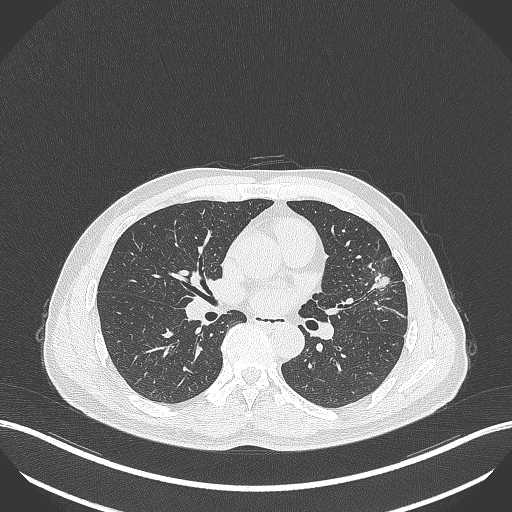
Chest CT, one axial slice; reconstruction kernel B70f; 120 kVp; lung window (W 1500 / L -600 HU); 1 mm slice thickness; 512 × 512 image matrix. Male patient, age 55 years. From the clinical record (not read from this slice): clinical TNM (as recorded): T1c N0 M0.
Annotated regions visible in this slice (rectangle marked by the reading radiologist):
- lung tumour (recorded histology: adenocarcinoma): bounding box (x1, y1, x2, y2) in pixels: (369, 267, 395, 296)